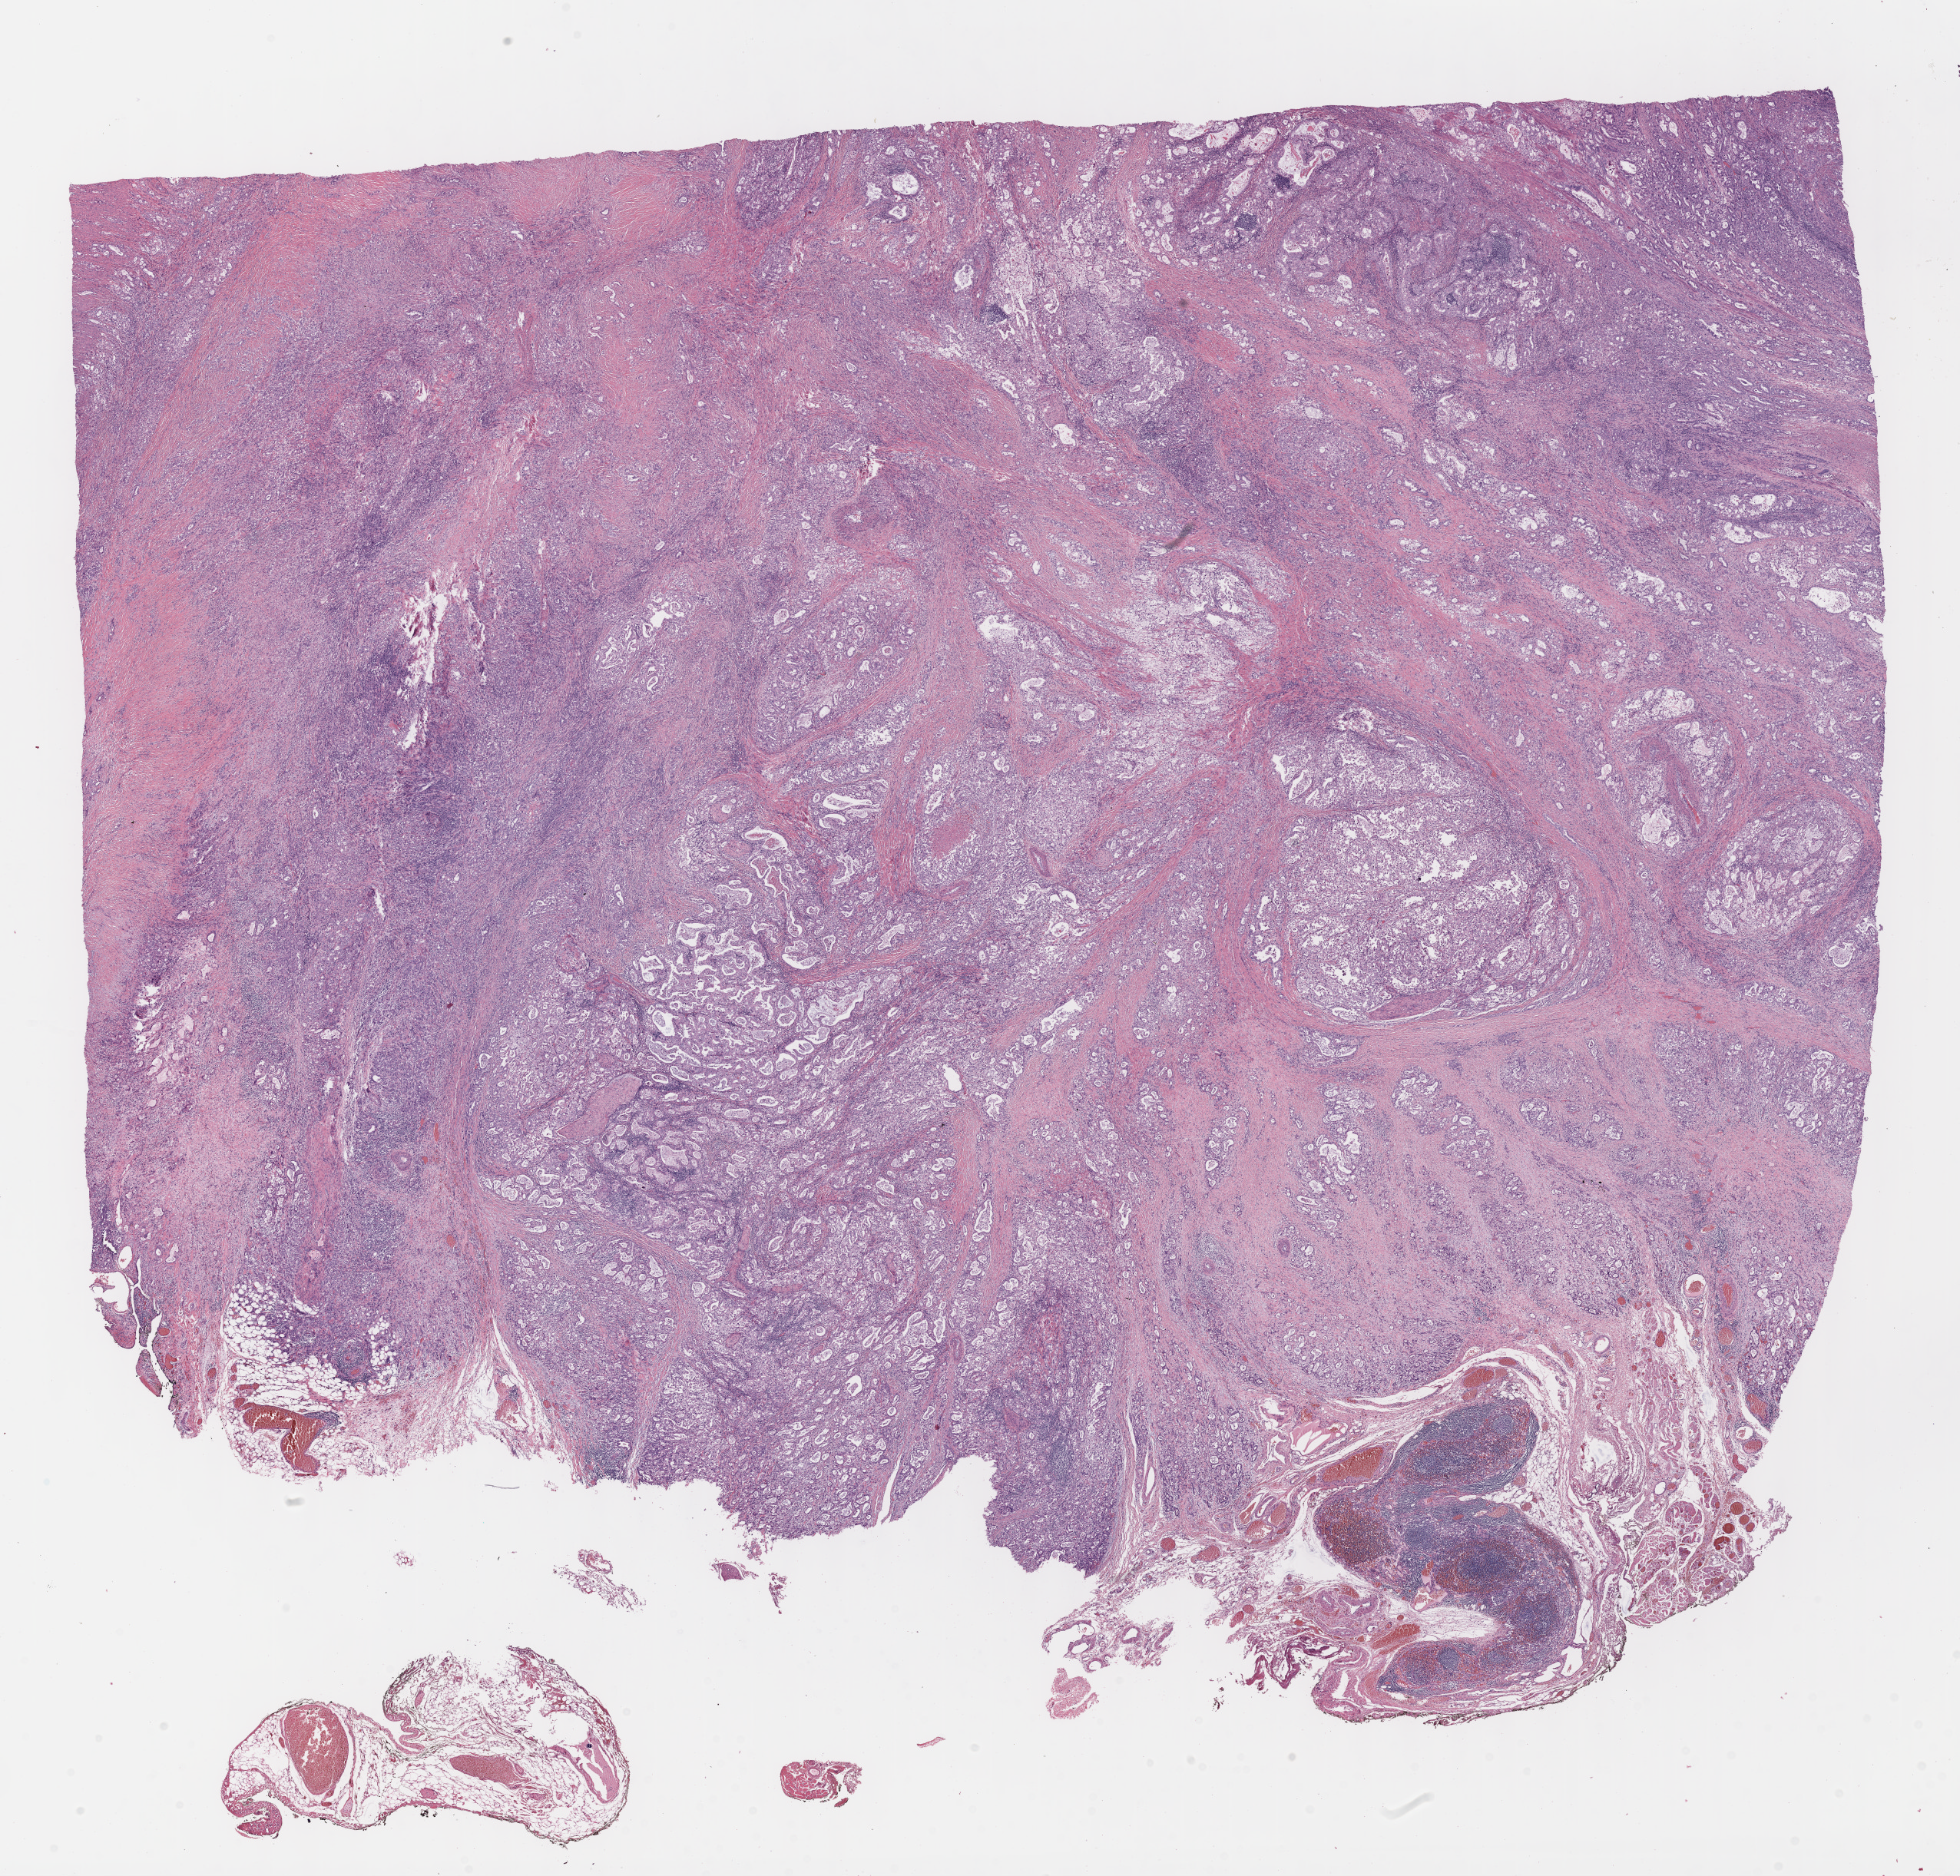
Digitized Hematoxylin and eosin (H&E) stained tissue section (whole slide) — shown as a low-resolution overview of the whole scanned area (about 20.6 x 19.7 mm, from a 40x scan), formalin-fixed paraffin-embedded (FFPE) diagnostic section, sample: primary tumour, stomach. Patient: male, age at initial diagnosis 57 years. Histologic grade: G2 (moderately differentiated).
Lymph nodes positive (case pathology): 1 of 14 examined. AJCC pathologic stage: IIB (7th edition). Histologic diagnosis: Adenocarcinoma, NOS (cardia, NOS).